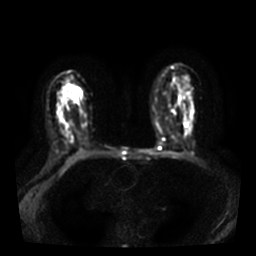
Breast MRI, one axial slice; diffusion-weighted series; image 2 of 4 stored at this slice position (different b-values; order by instance number); 3 T; 5 mm slice thickness; 256 × 256 image matrix, field of view 320 × 320 mm. Female patient.
Annotated regions visible in this slice (manually delineated by an expert):
- tumour on diffusion-weighted imaging: bounding box <73,93,77,98> (left, top, right, bottom; pixels)